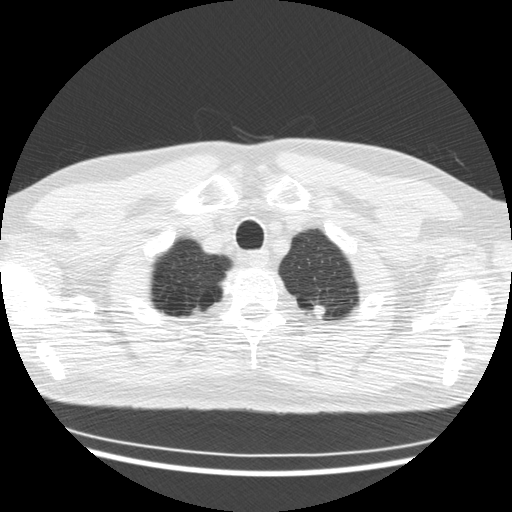
Low-dose screening chest CT, axial slice. Second screening round (one year after baseline). Lung window (W 1500 / L -600 HU). 512 × 512 image matrix, field of view 360 × 360 mm. Male participant, aged 57 years at enrolment. Former smoker at enrolment.
Lesion marked by an expert reader, bounding box (x1, y1, x2, y2) in pixels: (304, 298, 333, 324). The screening reader recorded 2 non-calcified nodules or masses ≥4 mm on this exam; which of them this box marks is not recorded. Lung cancer was diagnosed 332 days after this screen: adenocarcinoma, NOS, left upper lobe, stage IV (AJCC 6th edition), 50 mm at pathology.